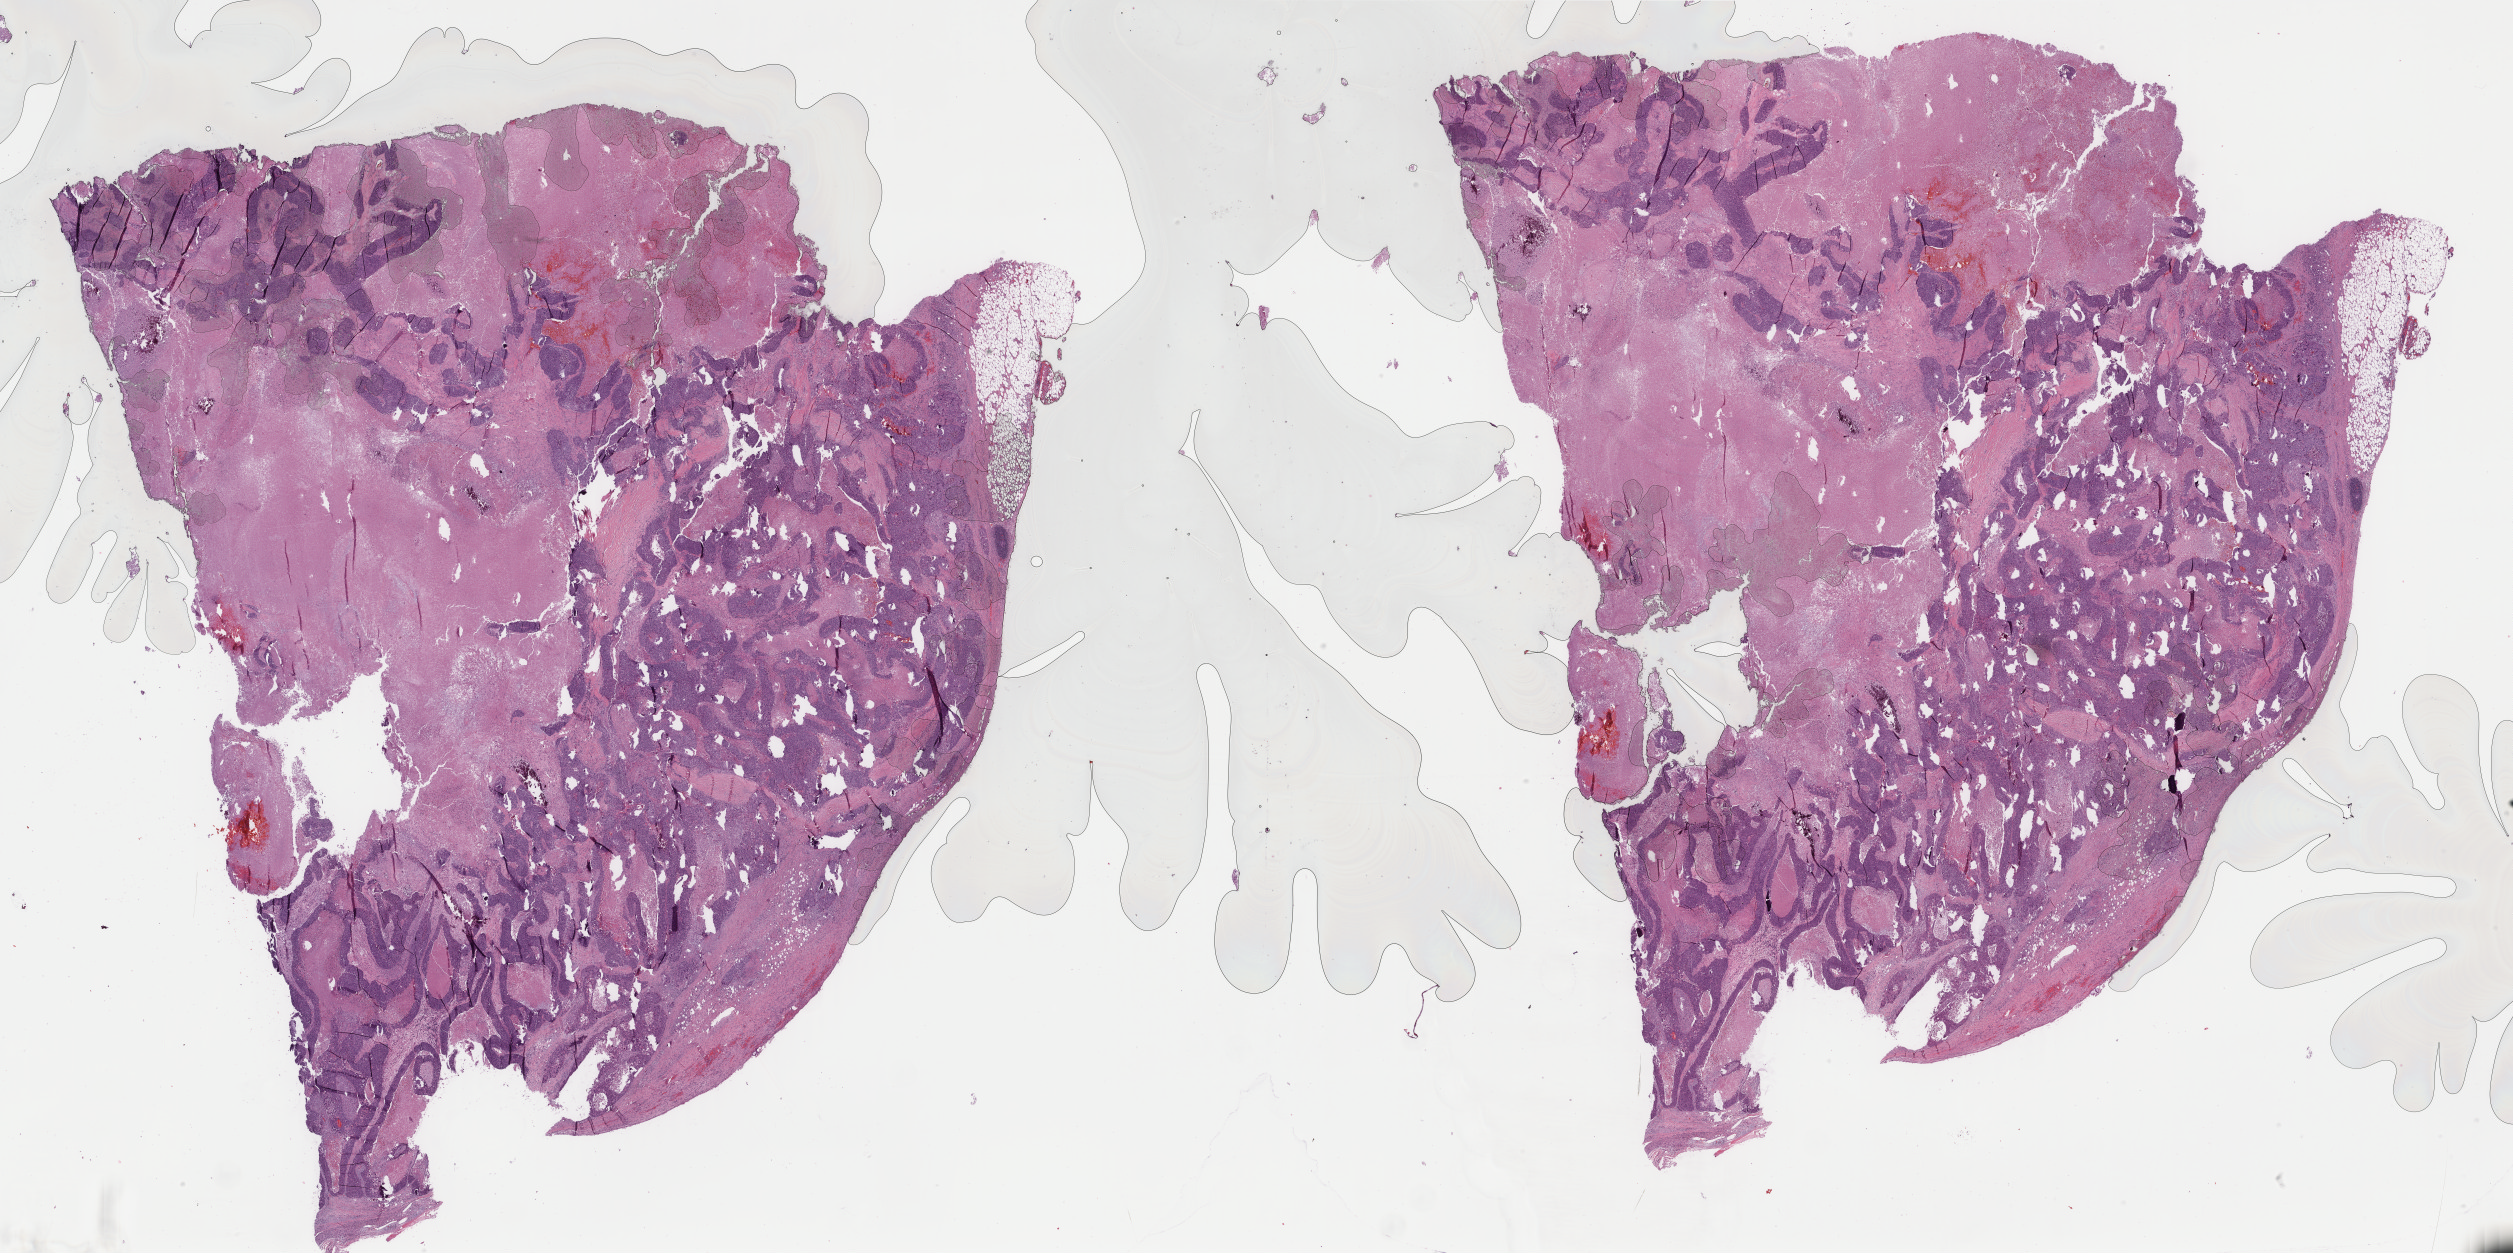
Whole-slide histology image, H&E-stained, whole scanned area (about 39.9 x 19.9 mm) shown as a low-resolution overview; formalin-fixed paraffin-embedded (FFPE) diagnostic section; sample: primary tumour, uterus. Female, age 69 years at initial diagnosis. Histologic grade: G3 (poorly differentiated).
FIGO stage: IVB. Pathologic diagnosis: Endometrioid adenocarcinoma, NOS (endometrium).